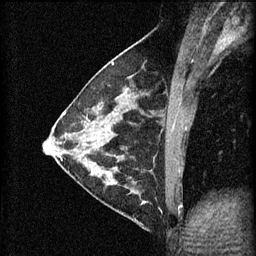
Breast MRI (dynamic contrast-enhanced), one sagittal slice; position 25 of 60 along the scan axis; 3 images stored at this slice position (order not interpretable as contrast timing); 1.5 T; TE 4.2 ms, TR 11 ms; 2 mm slice thickness; 256 × 256 image matrix, field of view 180 × 180 mm. Patient: female, 29 years.
Annotated regions visible in this slice (semi-automatically segmented with operator editing):
- analysis volume of interest (the breast-tissue region the enhancement analysis was run in; not a lesion): box from (x=105, y=172) to (x=171, y=227) px
- tumour enhancement mask (voxels above the 70 % enhancement threshold inside the analysis volume of interest): (x=135, y=182)–(x=147, y=205)